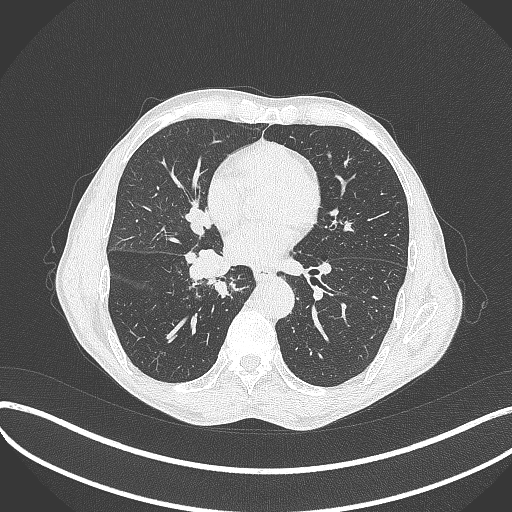
Chest CT, one axial slice. Slice 198 of 481 in the series (ordered by position). 120 kVp. Lung window (W 1500 / L -600 HU). 512 × 512 image matrix, field of view 400 × 400 mm. Male patient, age 65 years. Case-level facts recorded for this patient, not image findings: clinical TNM (as recorded): T2a N0 M0.
Annotated regions visible in this slice (rectangle marked by the reading radiologist):
- lung tumour (recorded histology: squamous cell carcinoma): bounding box [x1, y1, x2, y2] px = [178, 240, 235, 297]